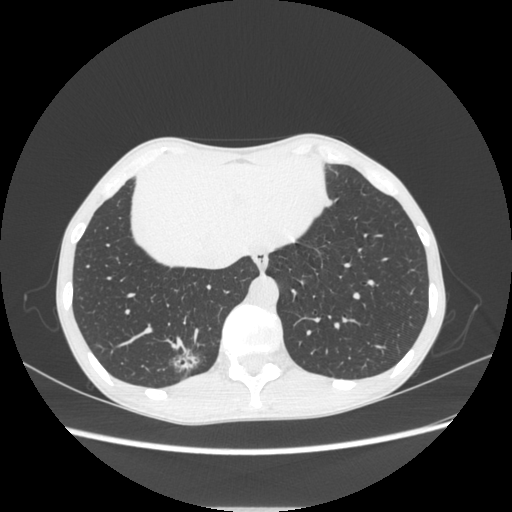
Chest CT, one axial slice; position 64 of 272 along the scan axis; reconstruction kernel STANDARD; 120 kVp; lung window (W 1500 / L -600 HU); 512 × 512 image matrix, field of view 350 × 350 mm. Patient: female, 51 years. From the clinical record (not read from this slice): clinical TNM (as recorded): T1c N0 M0; histopathological grade: G2-3.
Outlined on this slice (bounding box drawn by a radiologist):
- lung tumour (recorded histology: adenocarcinoma): bounding box [x1, y1, x2, y2] px = [160, 339, 210, 384]